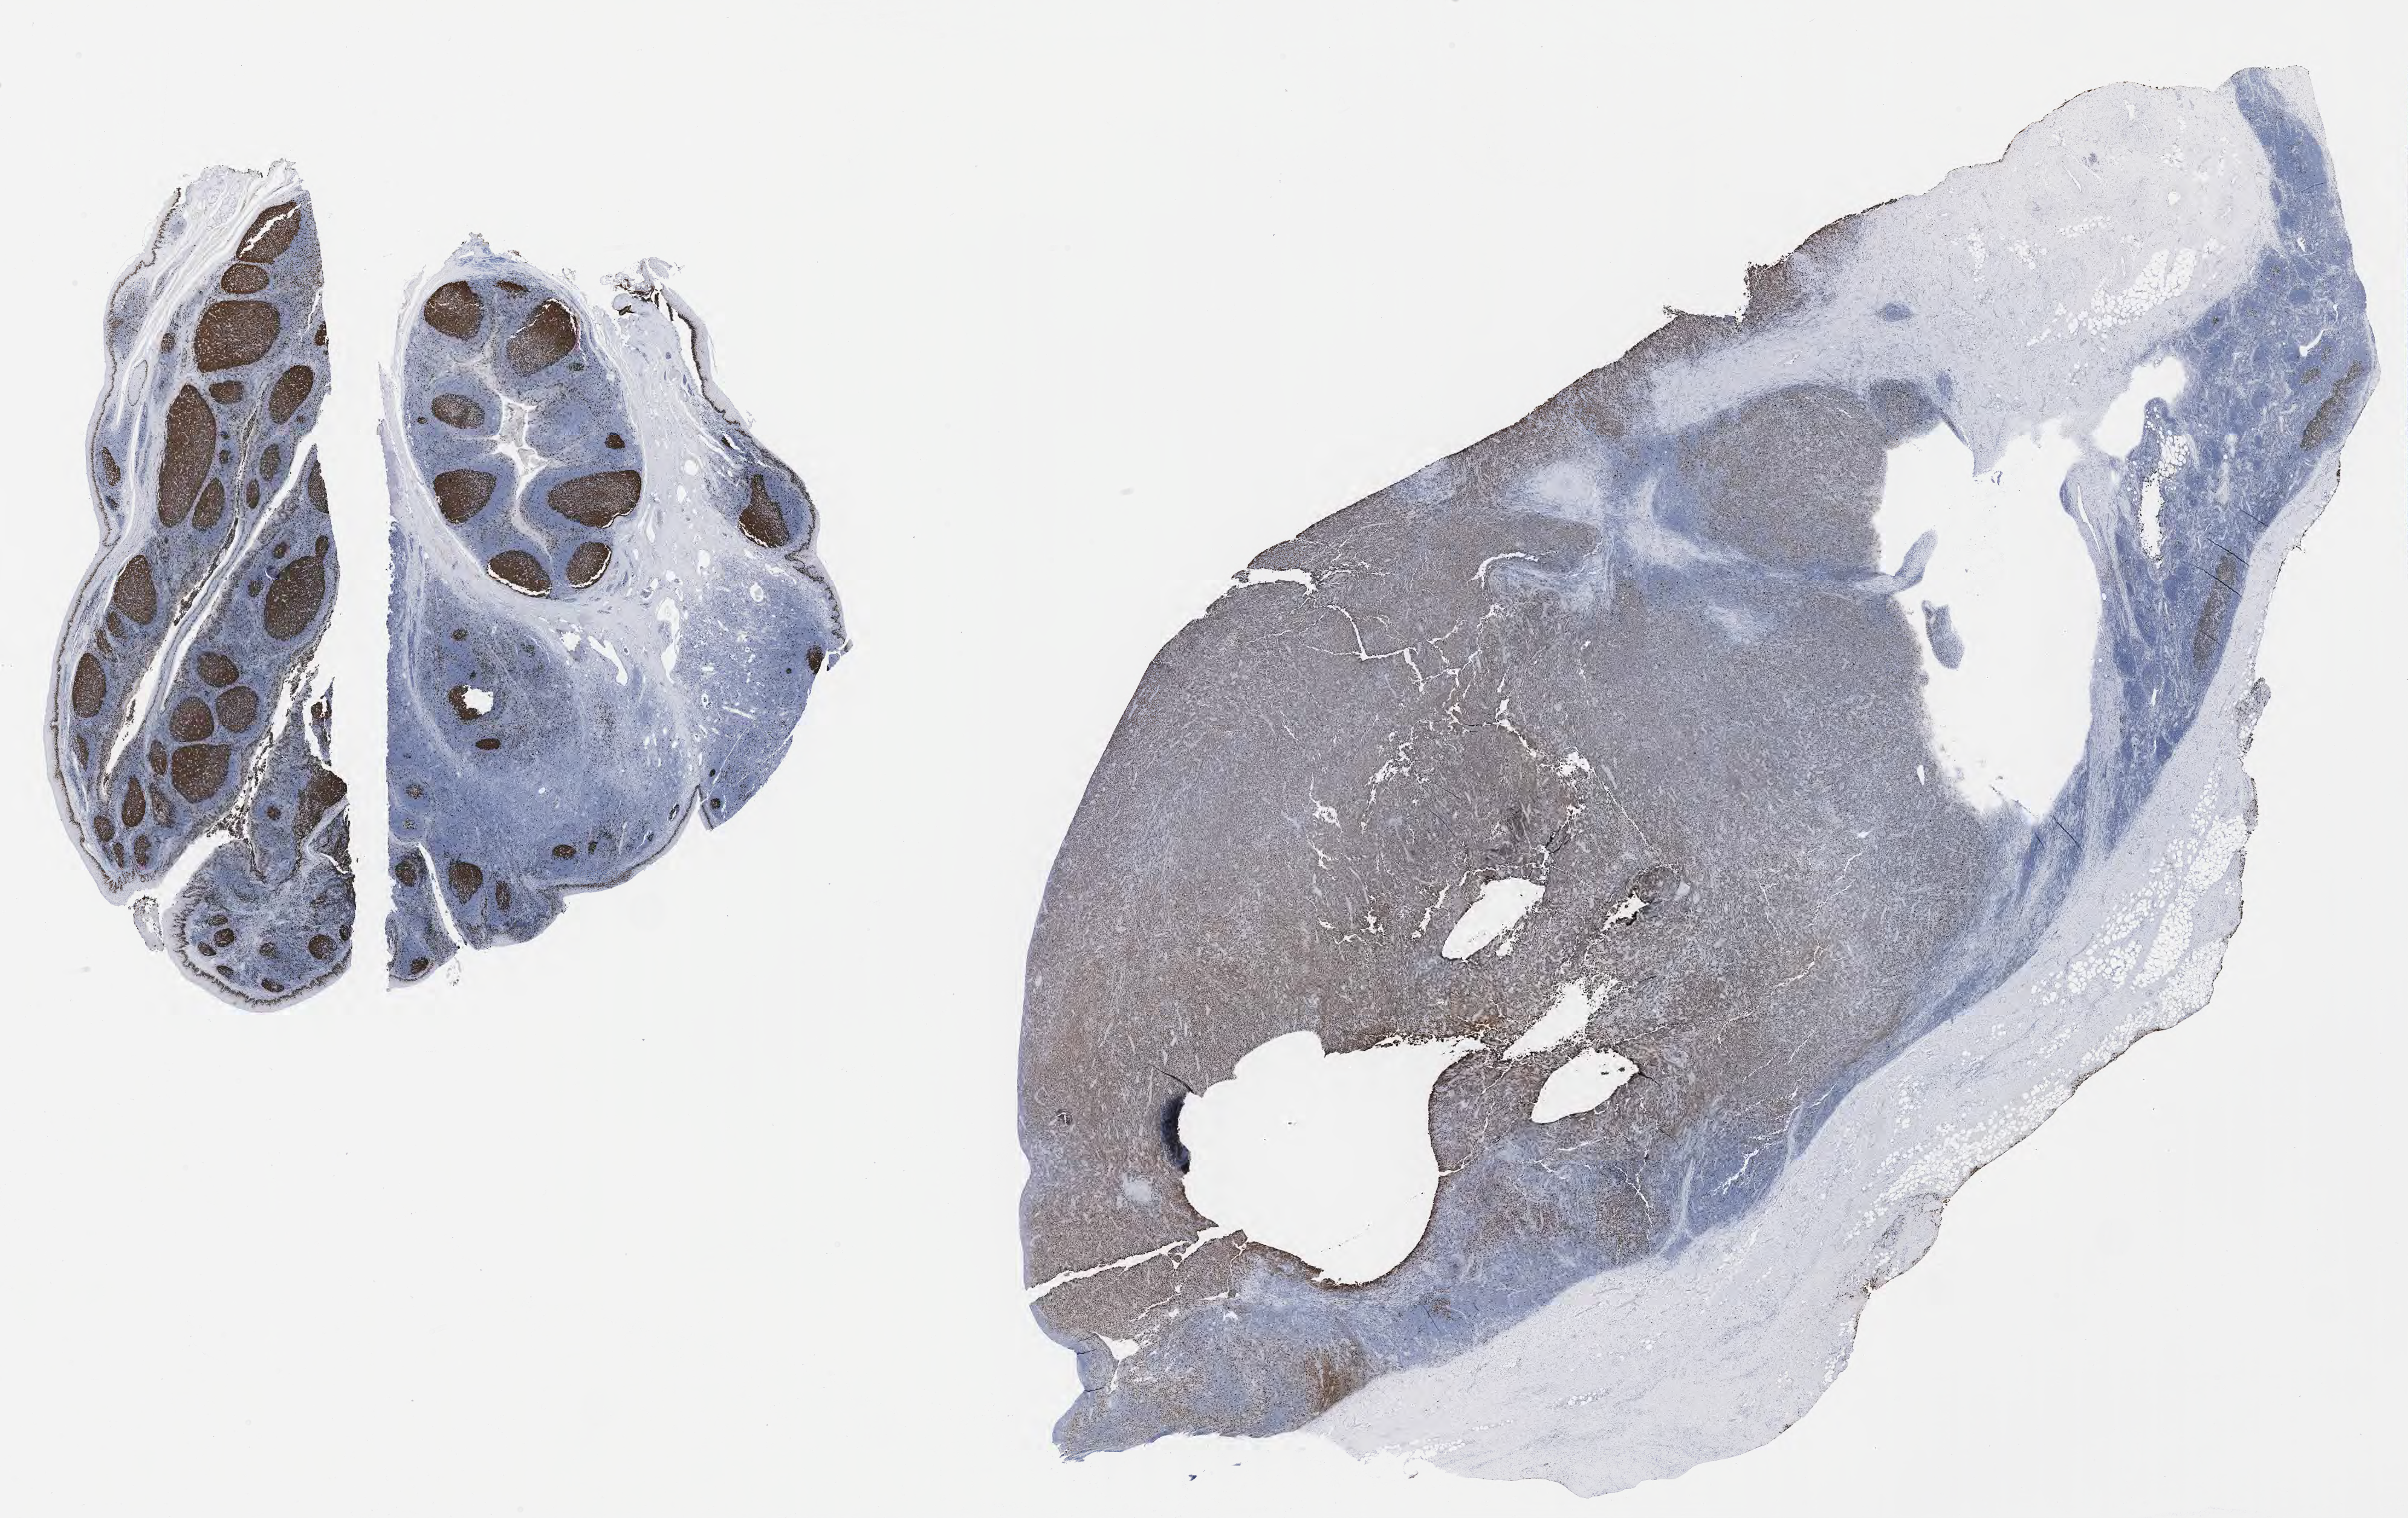
IHC for Ki-67, whole-slide image — whole scanned area (about 32.2 x 20.3 mm) shown as a low-resolution overview, tumor tissue, anatomic site: lymph node. Patient male; age 60 years.
Histologic diagnosis: Diffuse large B-cell lymphoma, NOS.